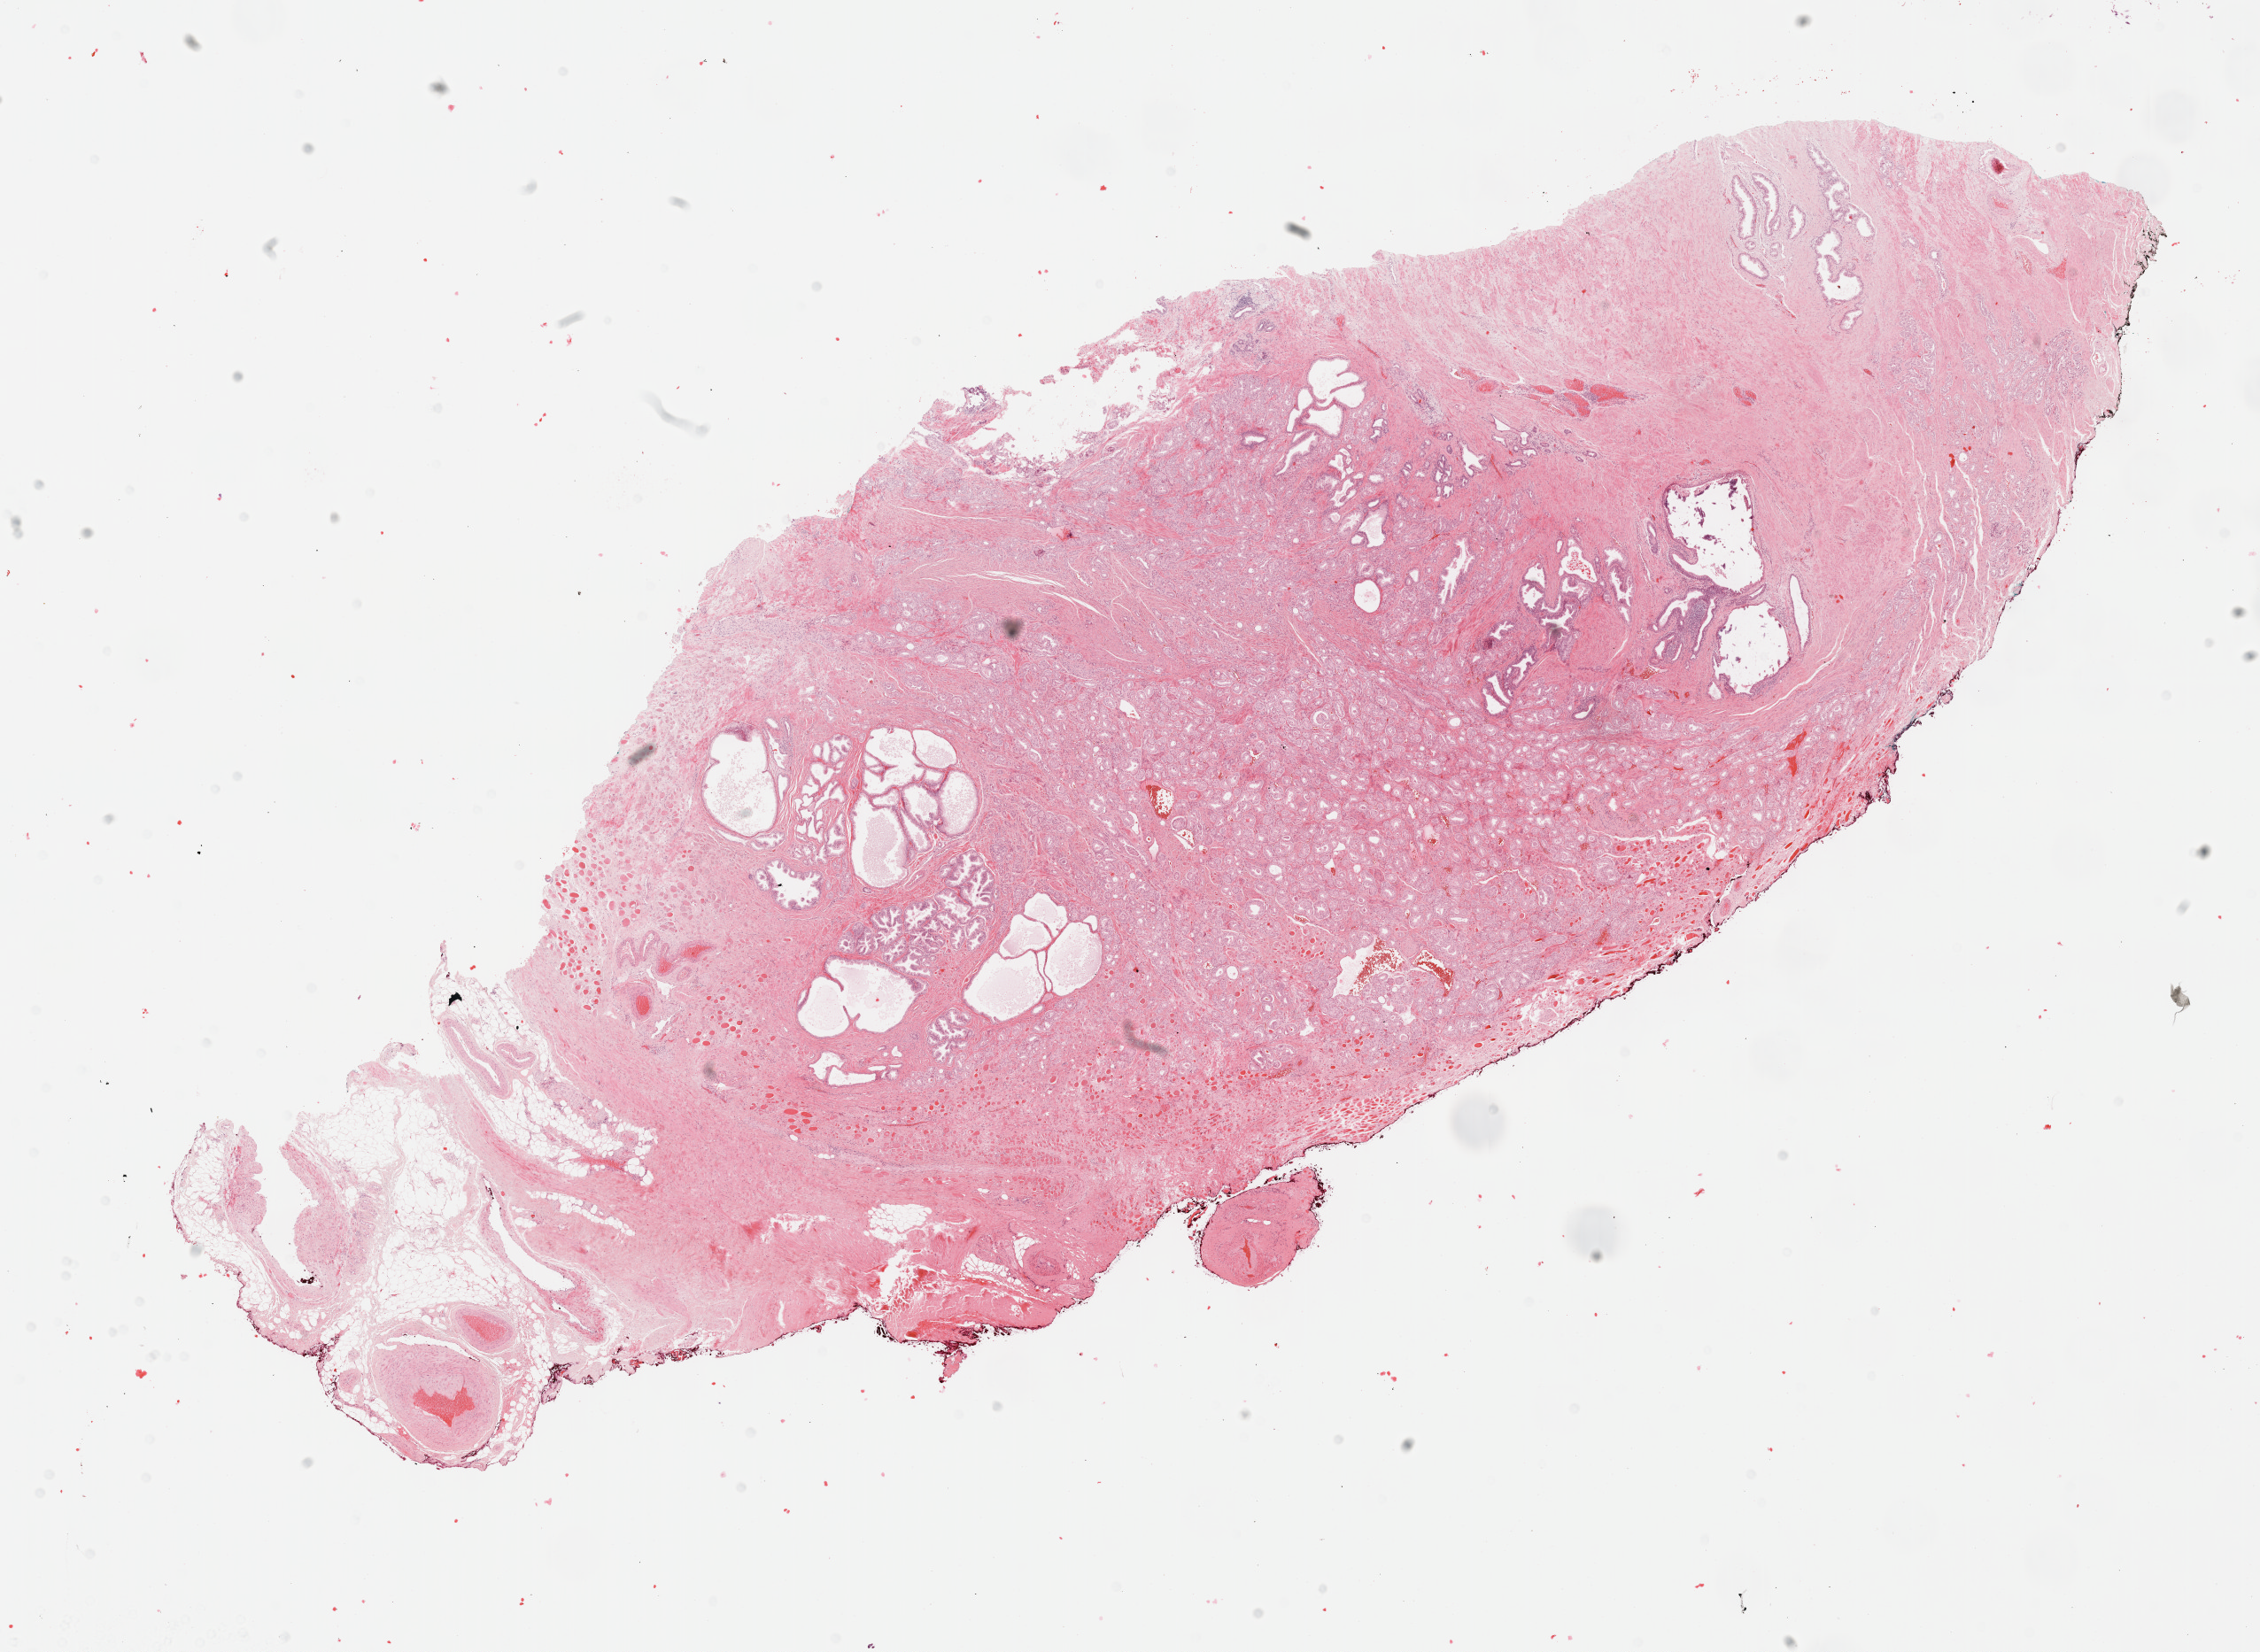
Whole-slide histology image, H&E — low-resolution overview of the scanned area, about 20.6 x 15.1 mm (from a 40x scan), FFPE section, prostate, primary tumour sample. Male patient; age at initial diagnosis 65 years. Gleason score: 6 (3+3).
Lymph nodes positive (case pathology): 0 of 5 examined. Laterality: right. Histologic diagnosis: Adenocarcinoma, NOS (prostate gland).